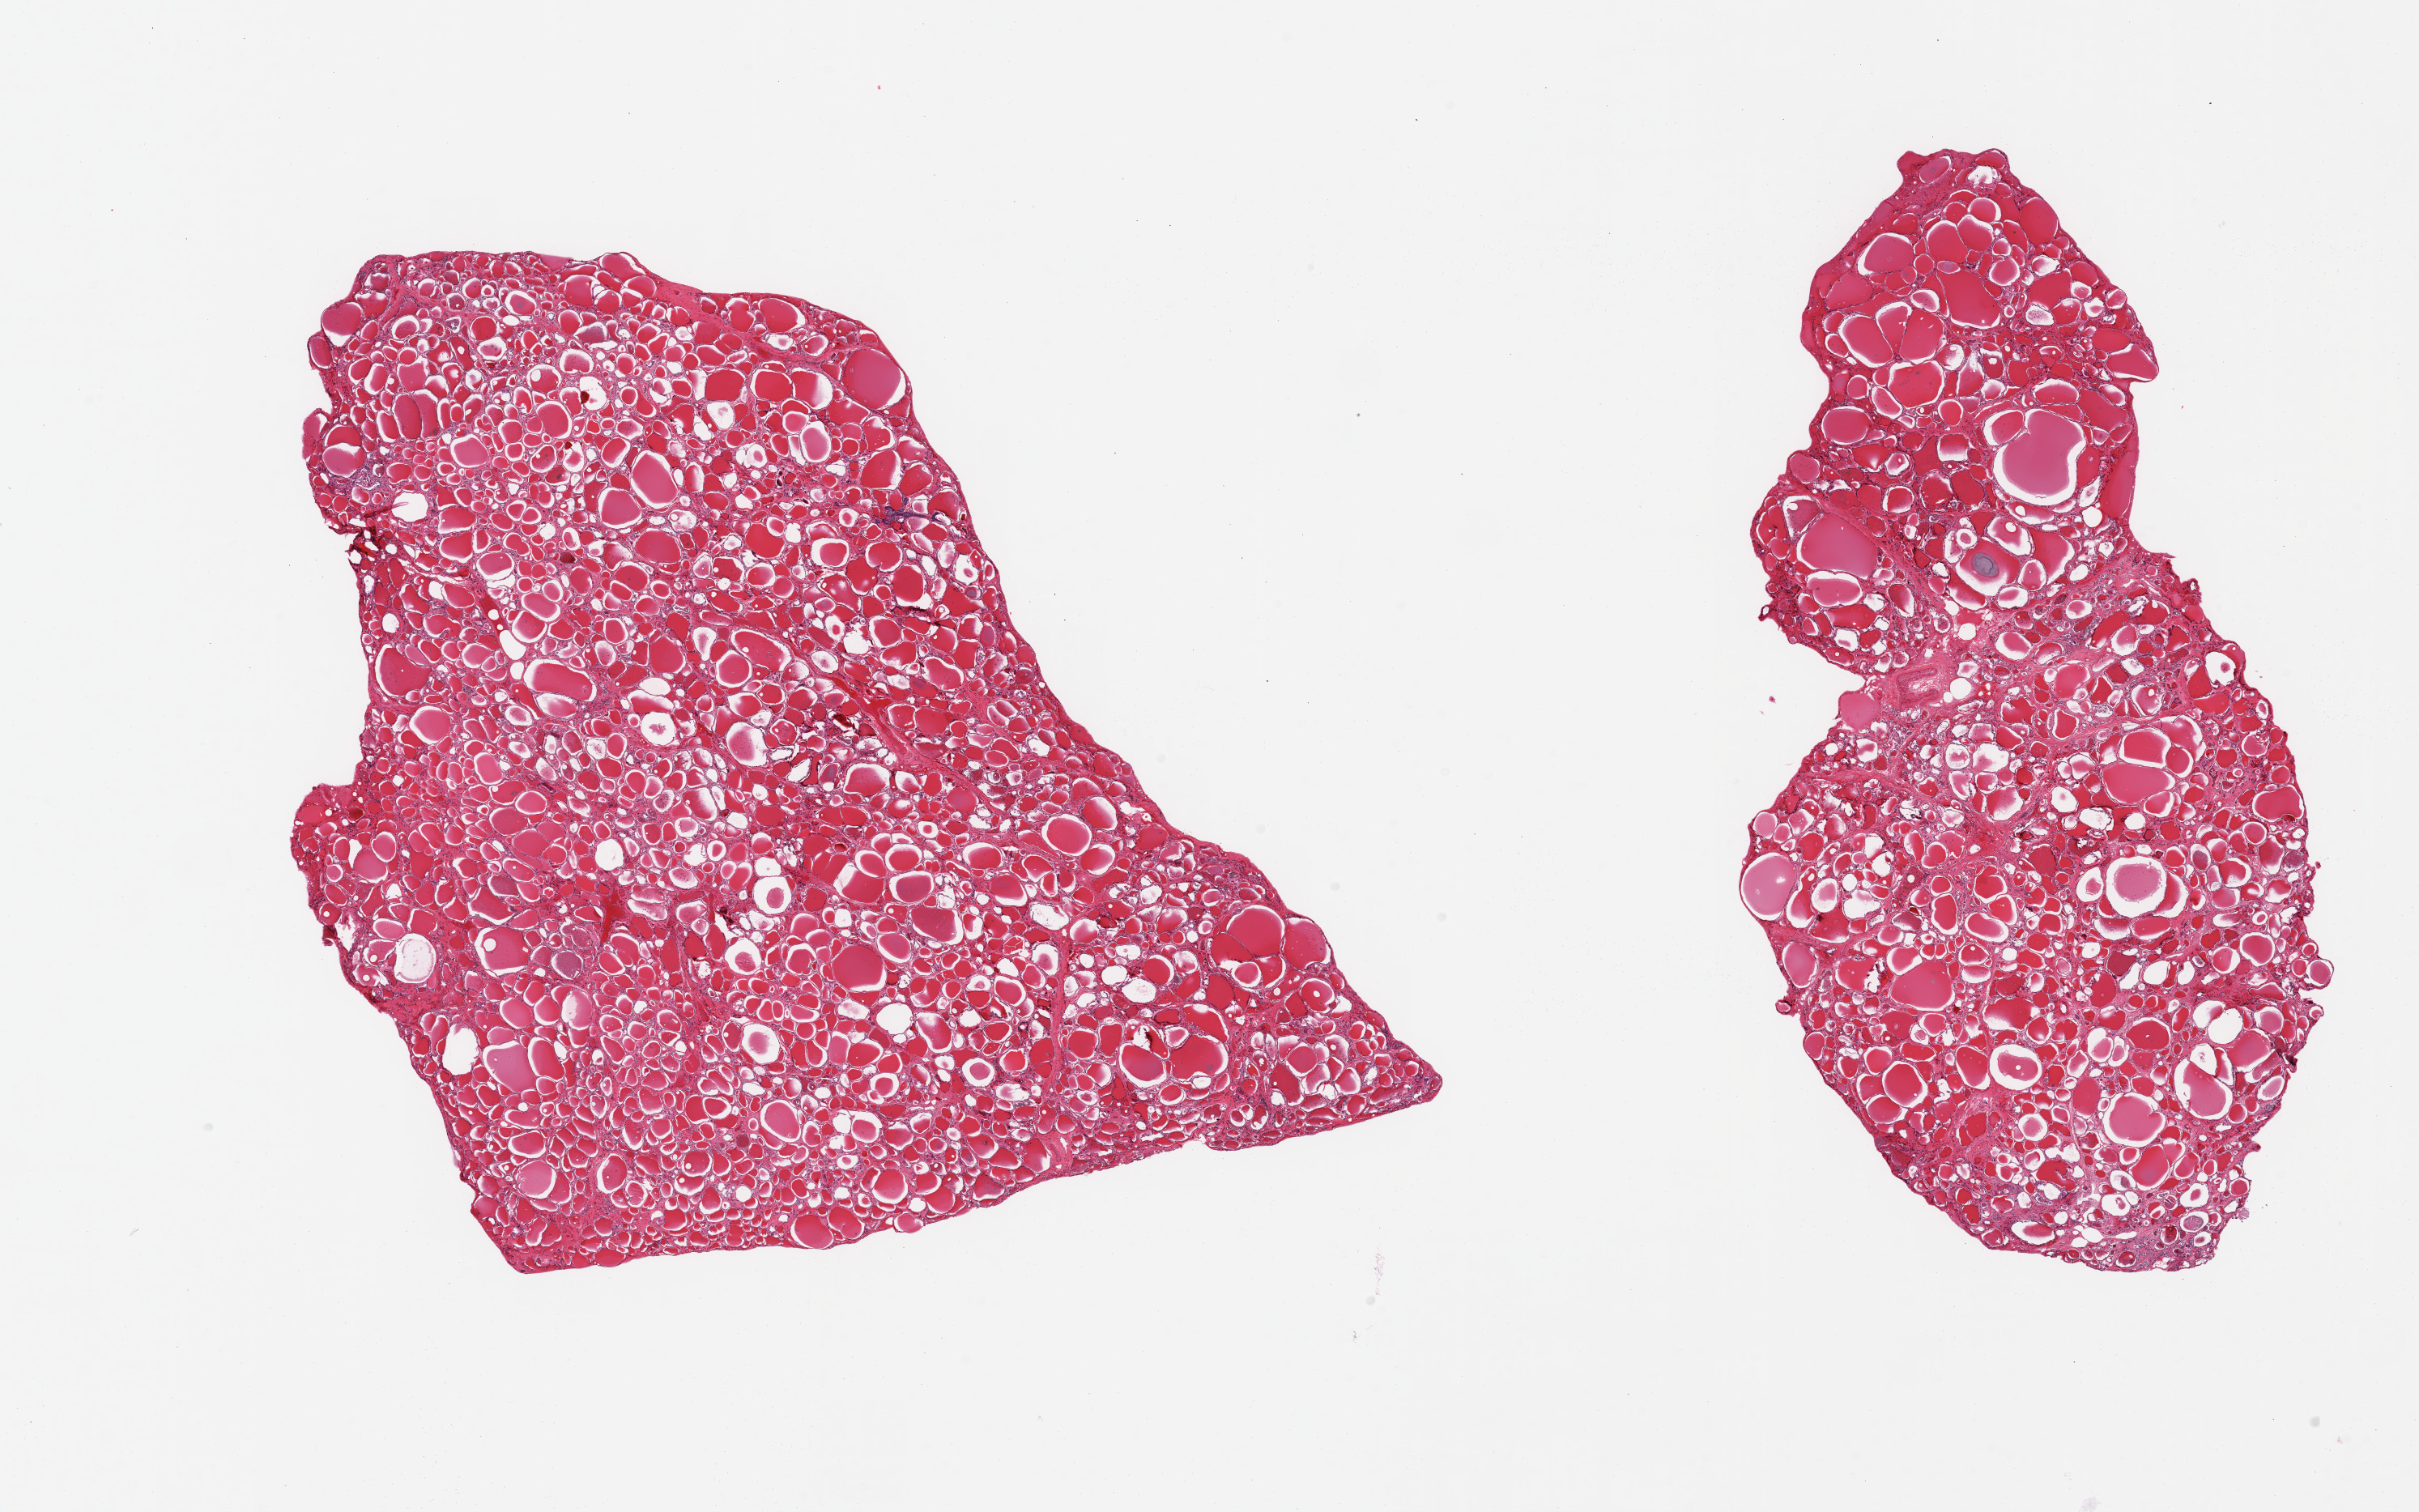
Hematoxylin and eosin (H&E) whole-slide image — a low-resolution overview of the entire scanned area, about 23.6 x 14.8 mm. PAXgene-fixed, paraffin-embedded tissue. Section of thyroid (target tissue). Tissue donor sample. Donor: male.
Pathologist's review note for this sample: 2 pieces, no abnormalities.